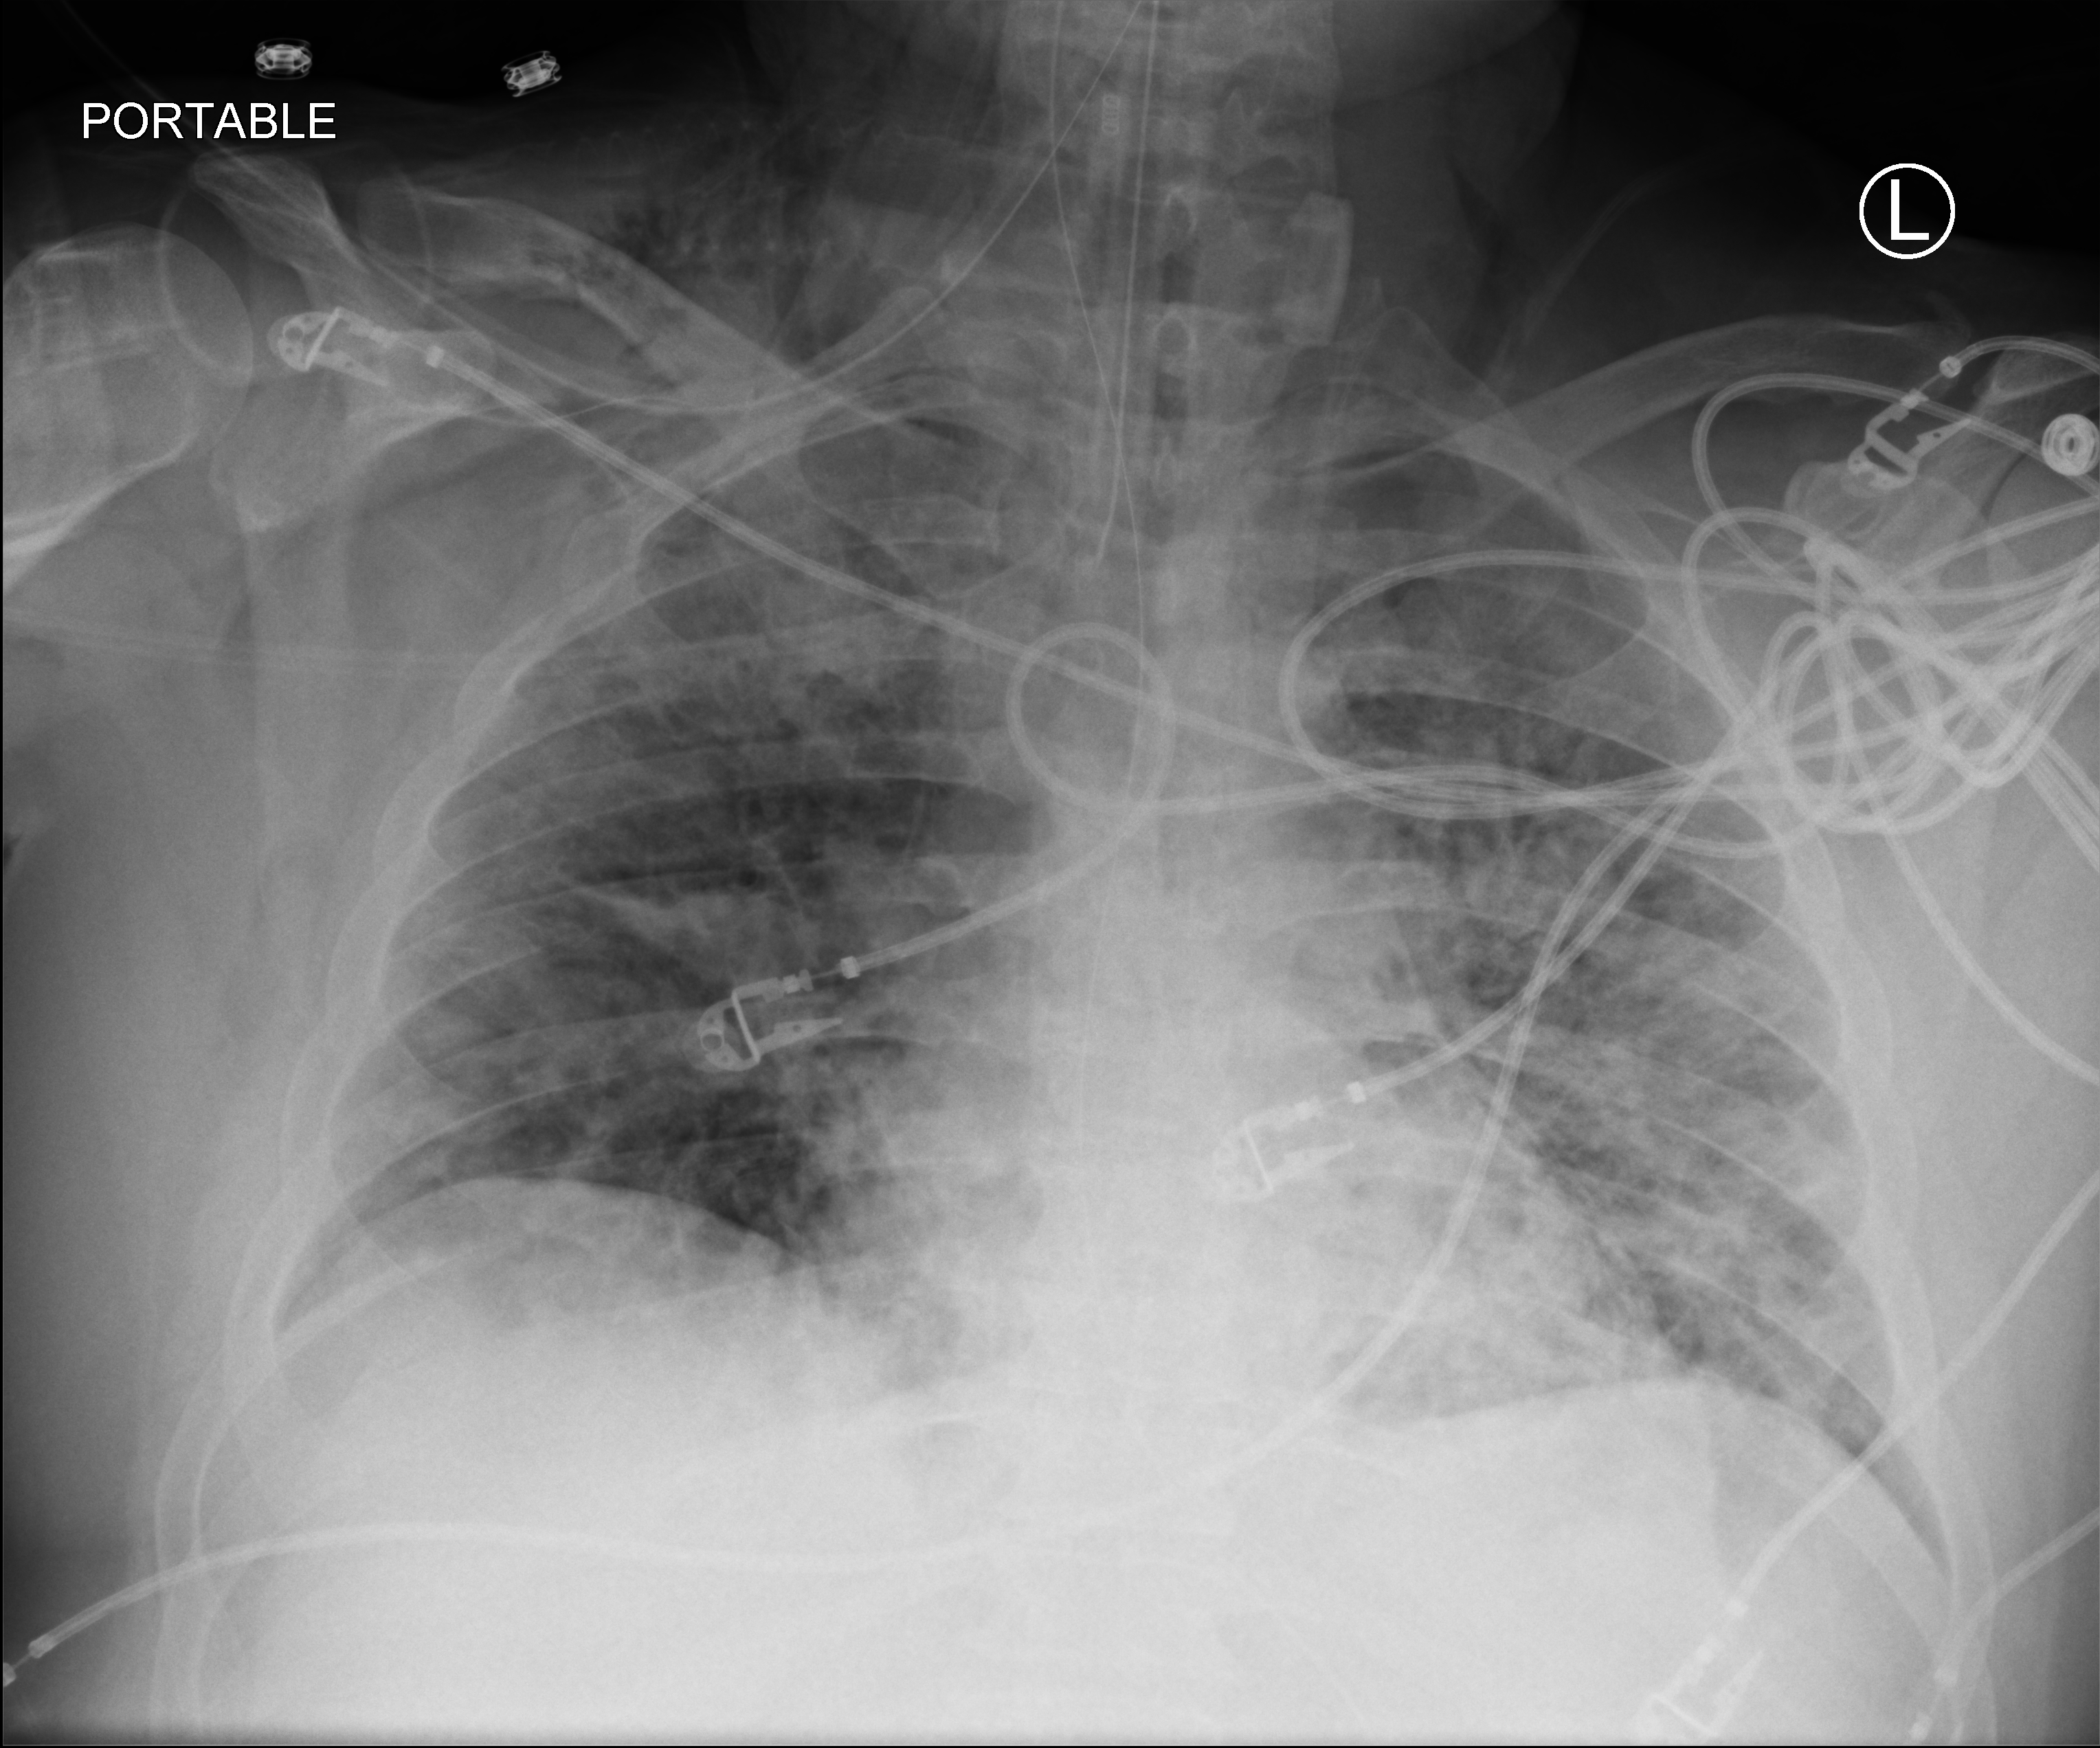
Chest X-ray (portable); anteroposterior (AP) projection. Adult patient hospitalised with COVID-19, age 18–59 years.
Hospital-stay facts (about this admission, not read from this image; timing relative to this image not recorded): mechanically ventilated during this hospital stay: yes.